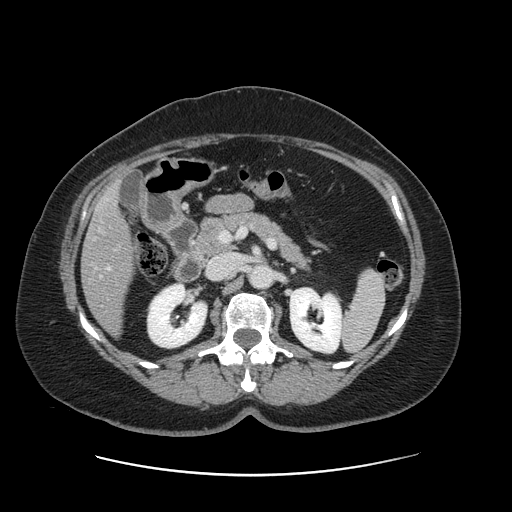
Contrast-enhanced abdominal CT, one axial slice. Position 65 of 161 along the scan axis. 120 kVp. Soft-tissue window (W 400 / L 40 HU). 512 × 512 image matrix, field of view 398 × 398 mm. Female patient, age 62 years. From the clinical record (not read from this slice): diagnosis: colorectal cancer liver metastases, imaged before liver resection; multiple liver metastases: no; largest metastasis: 2.5 cm; chemotherapy before resection: yes.
Annotated regions visible in this slice (outlined manually by an expert reader):
- liver: bounding box <82,188,133,333> (left, top, right, bottom; pixels)